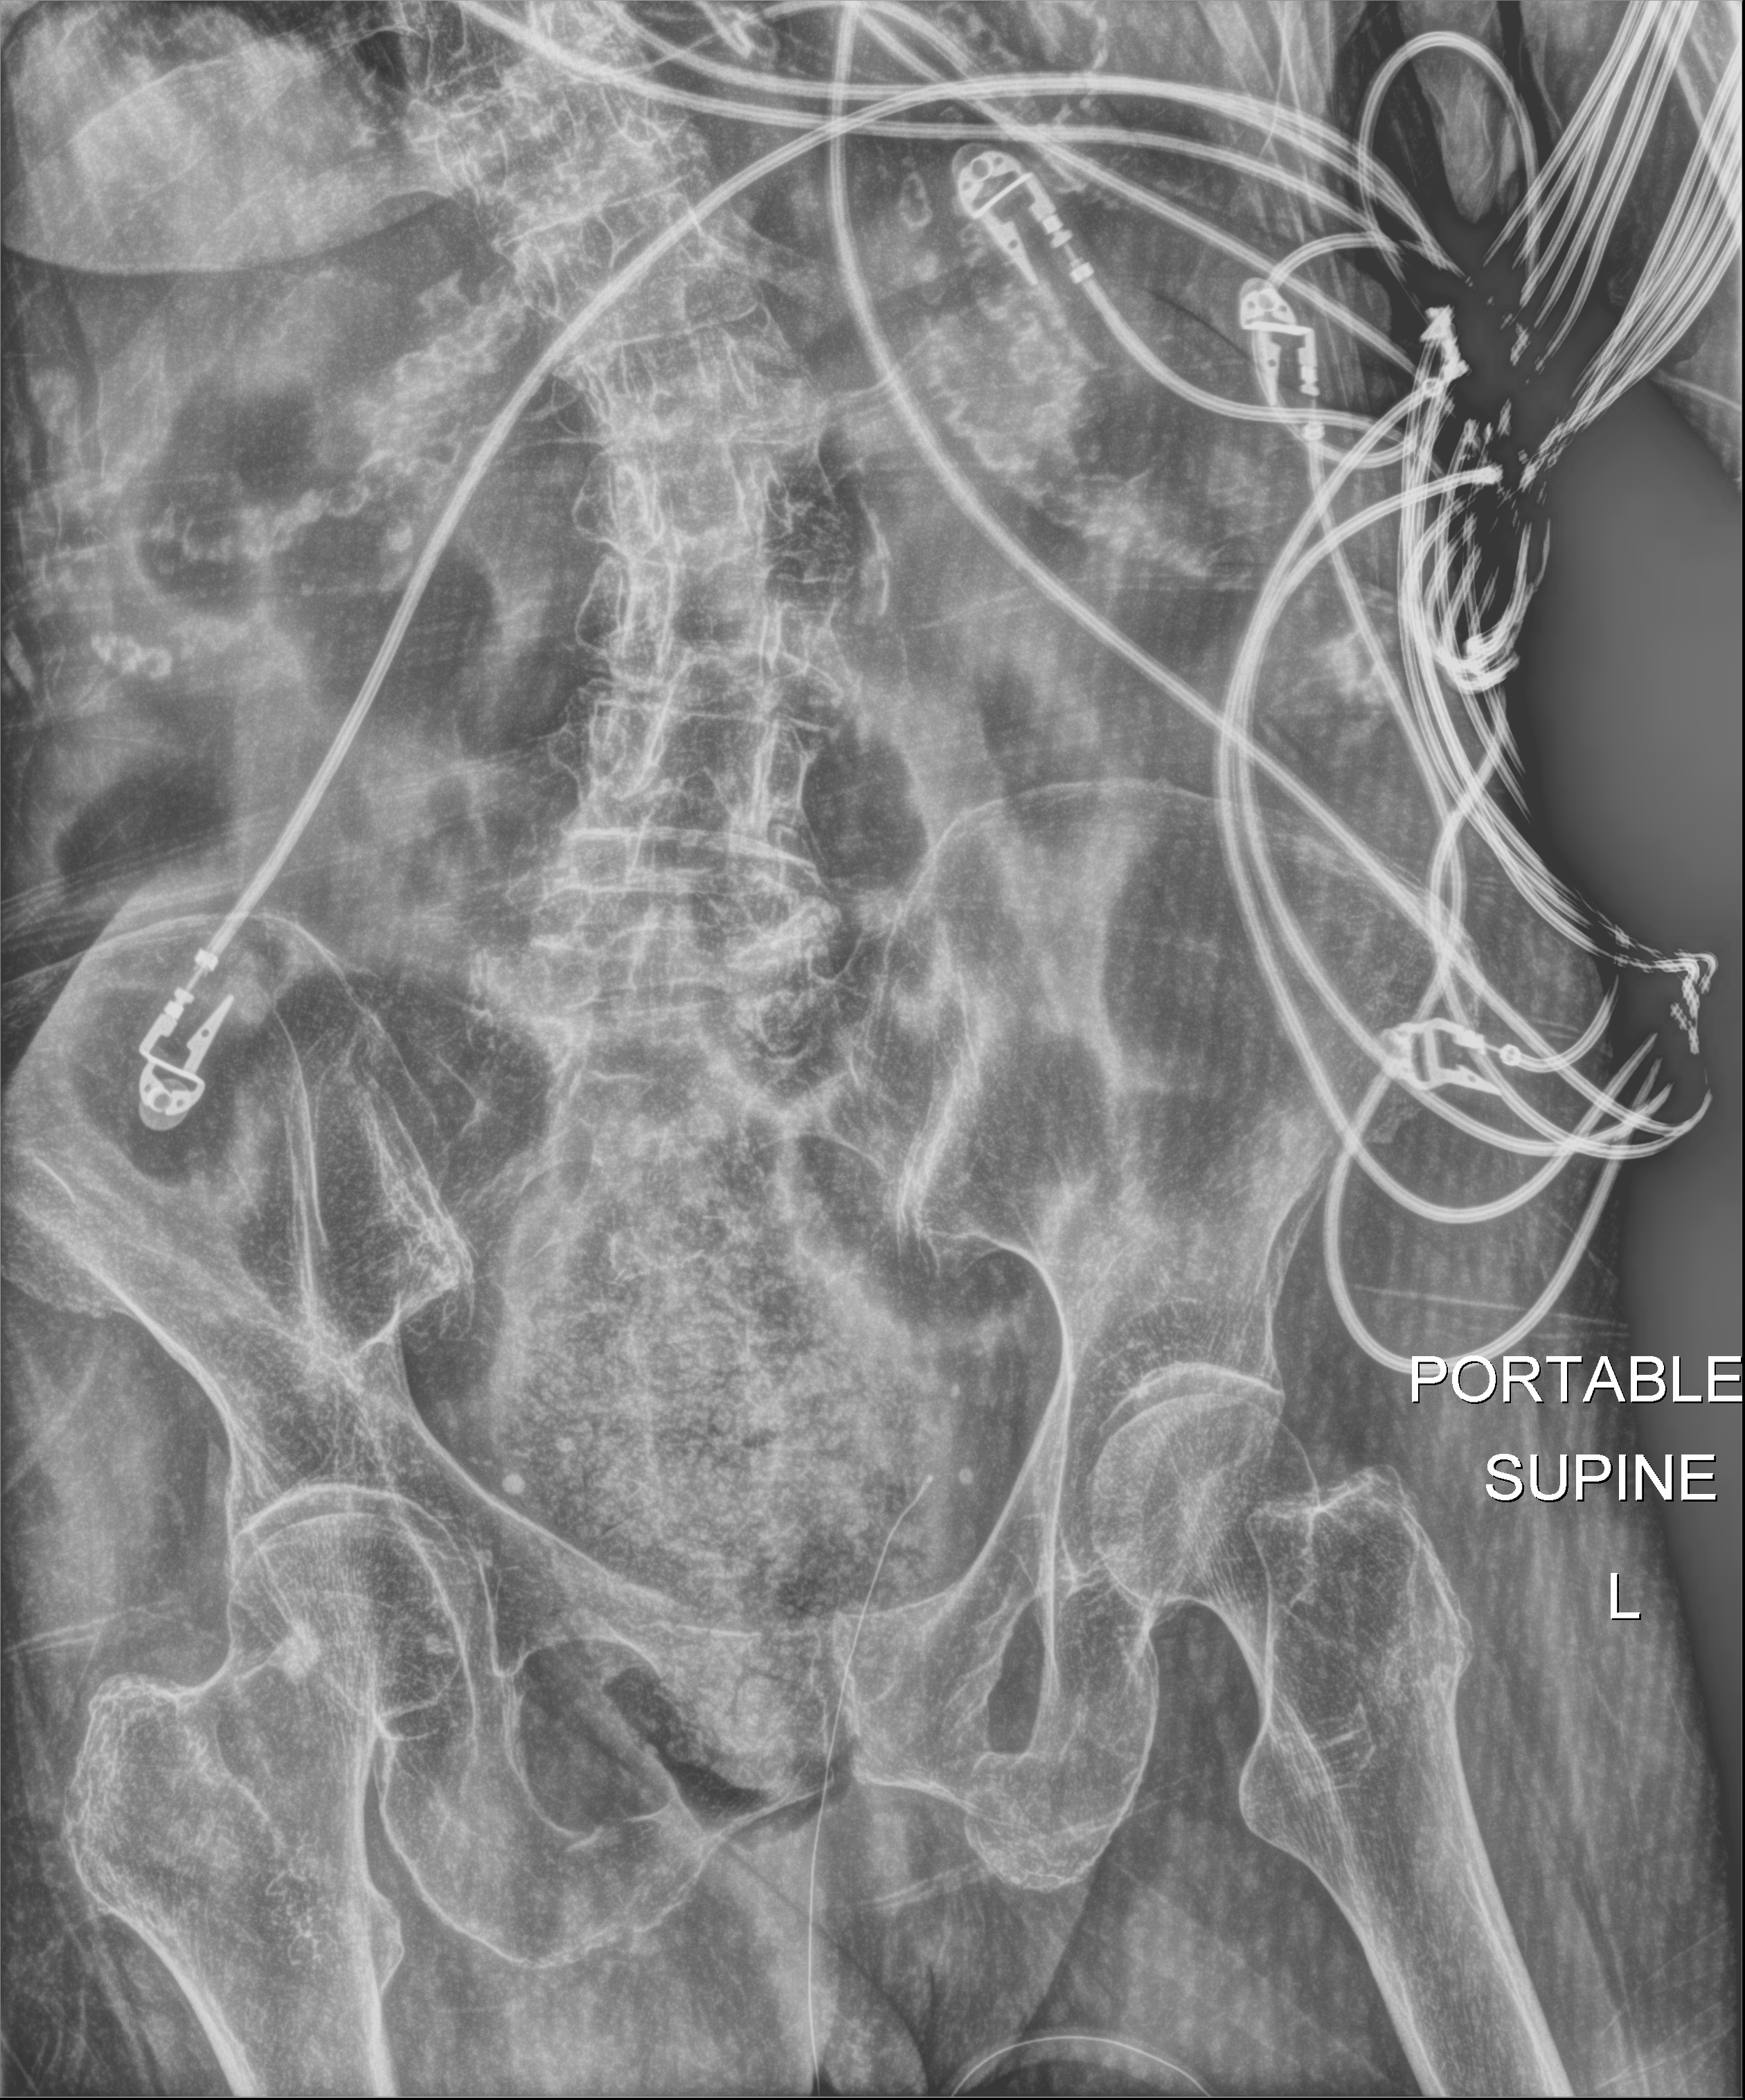
Portable abdomen radiograph. Female patient hospitalised with COVID-19, age 75–90 years.
From the hospital-stay record, not from the radiograph (when in the stay this image was taken is not recorded): admitted to intensive care during this hospital stay: no.